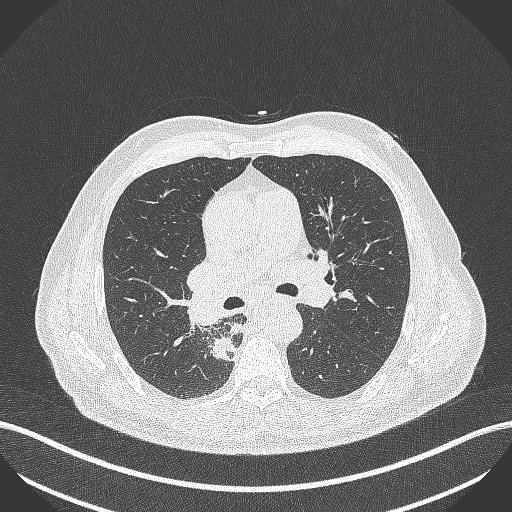
Chest CT, one axial slice; slice 277 of 451 in the series (ordered by position); 100 kVp; lung window (W 1500 / L -600 HU); 1 mm slice thickness; 512 × 512 image matrix, field of view 400 × 400 mm. Male patient, age 61 years. Case-level facts recorded for this patient, not image findings: clinical TNM (as recorded): T1 N0 M0; histopathological grade: G3.
Structures marked on this image (bounding box drawn by a radiologist):
- lung tumour (recorded histology: small cell carcinoma): bounding box [x1, y1, x2, y2] px = [211, 336, 240, 361]